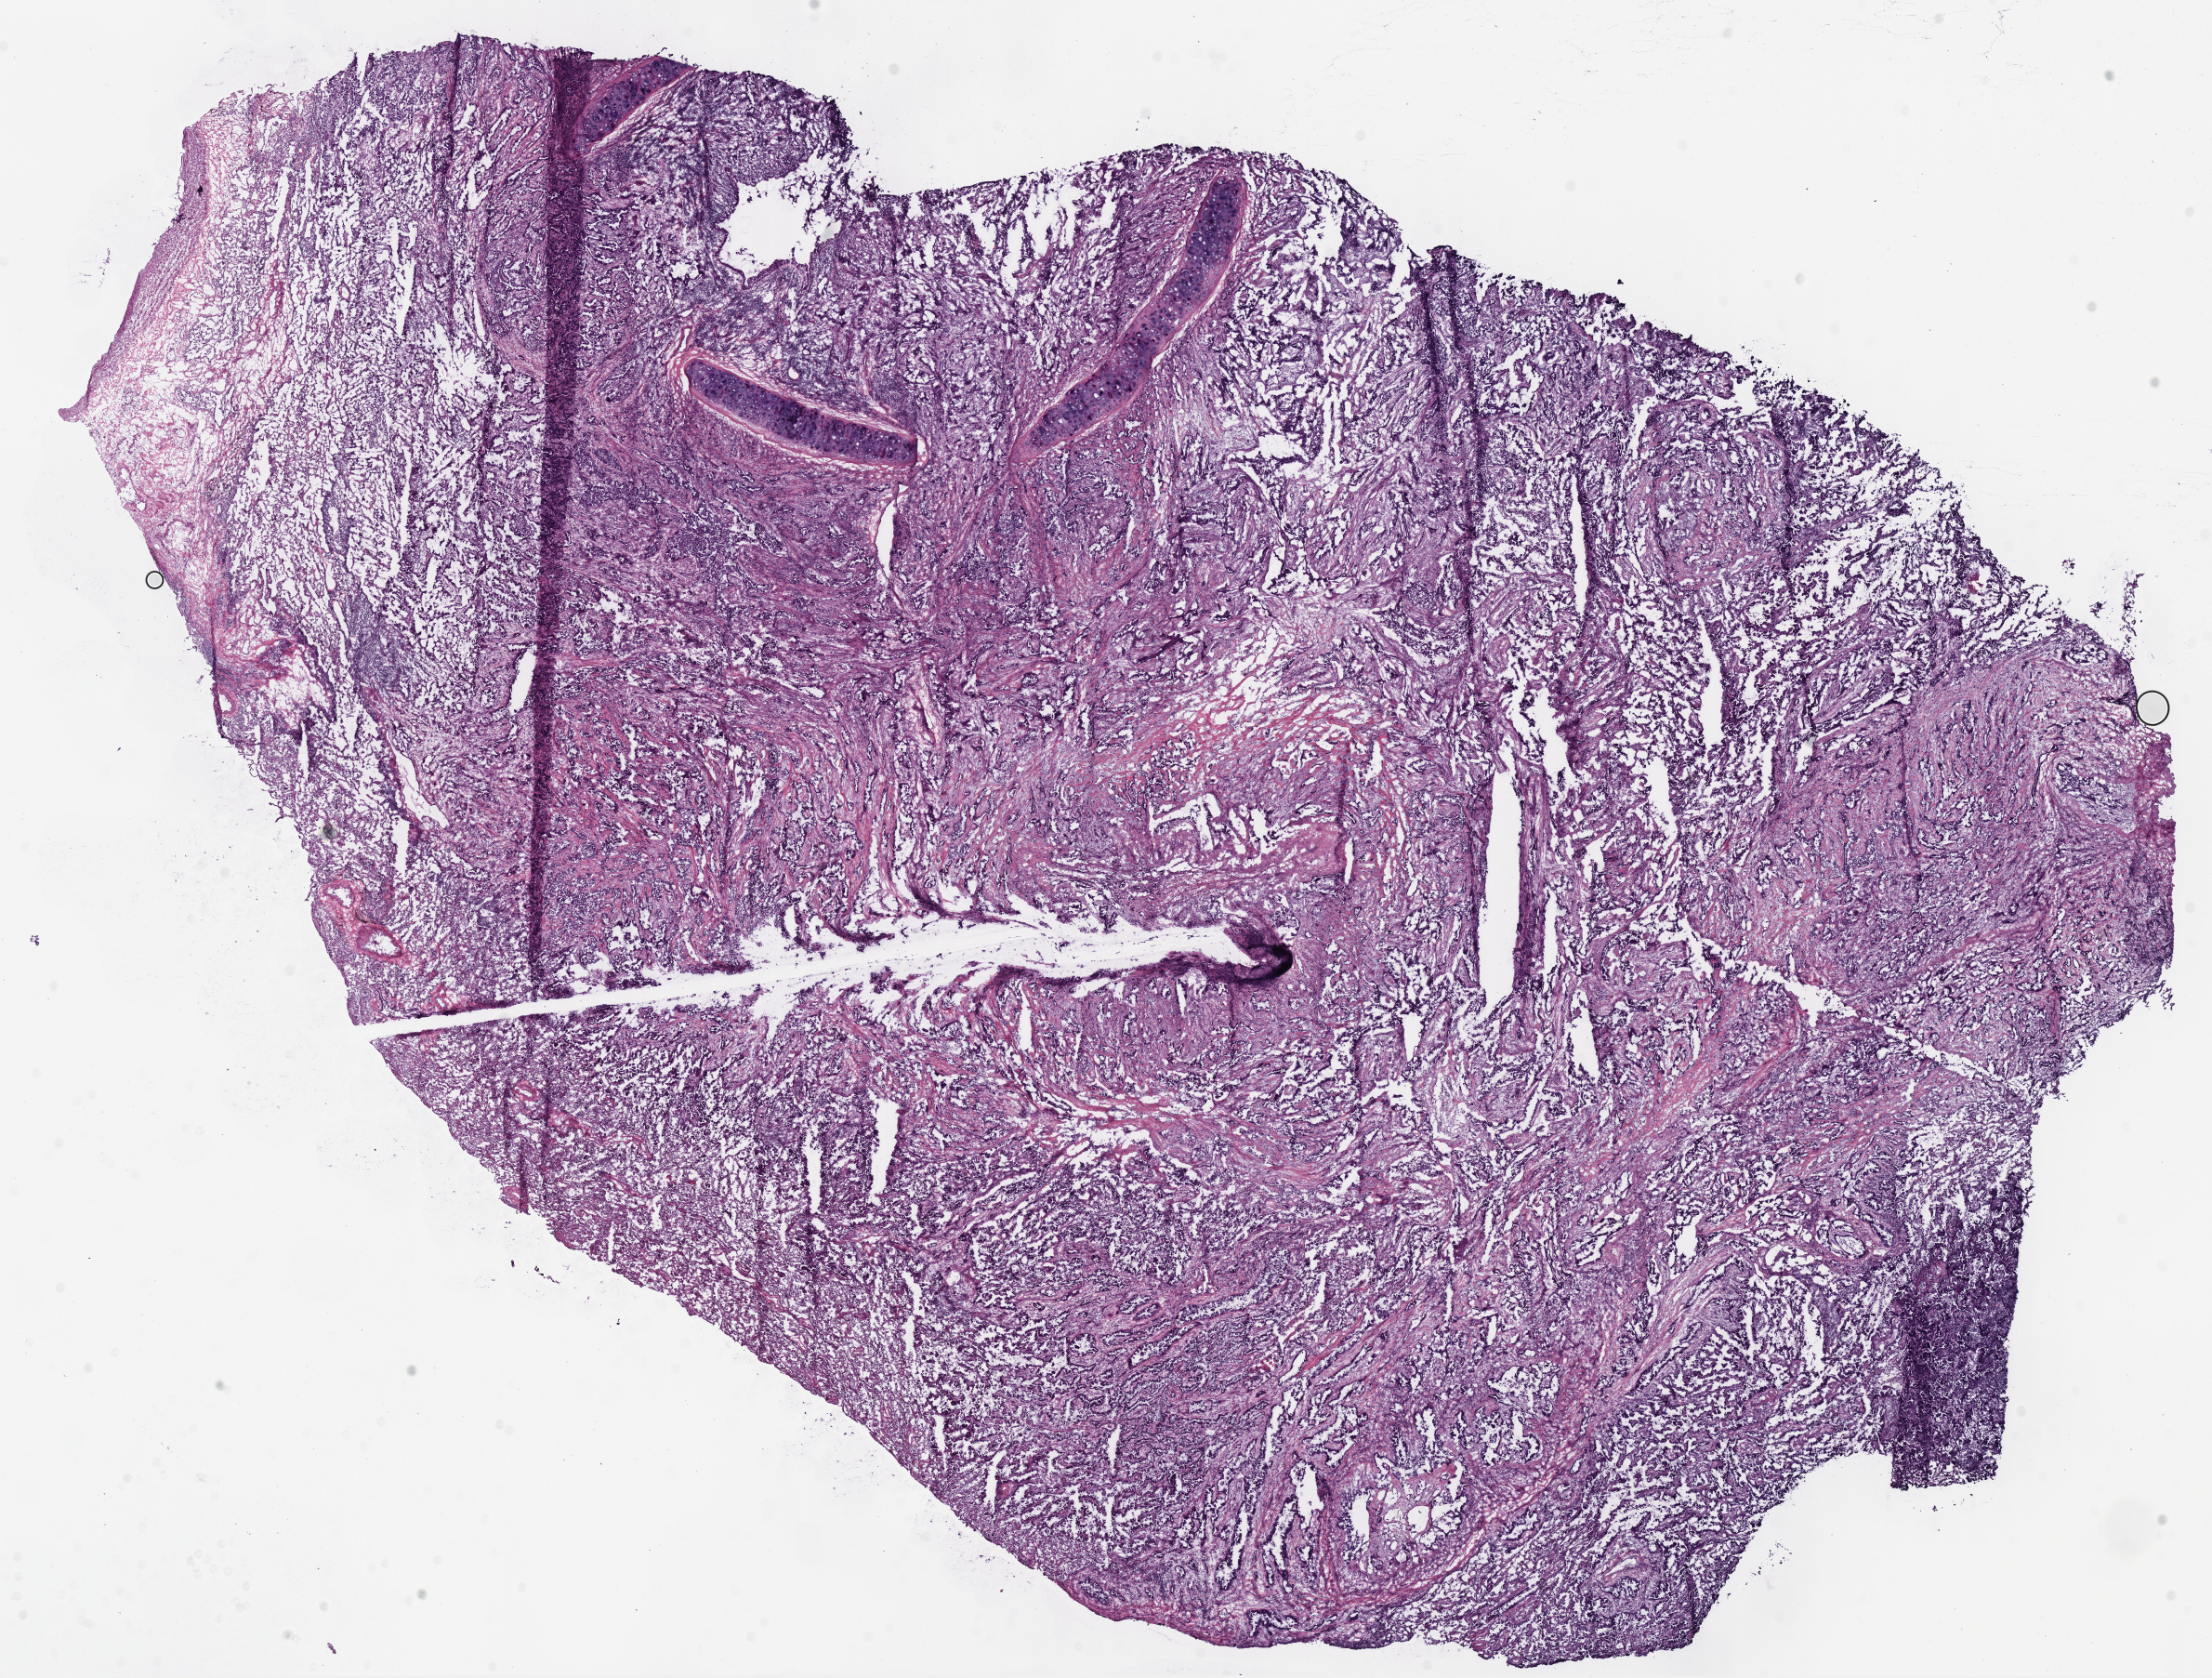
Hematoxylin and eosin (H&E) stained whole-slide image, a low-resolution overview of the entire scanned area, about 18.8 x 14.2 mm (from a 40x scan), frozen section, primary tumour sample from the lung. Patient: female, age at initial diagnosis 62 years. Slide review estimates, as recorded: tumour cells 96%, tumour nuclei 80%, normal cells 2%, stromal cells 0%, necrosis 2%. Inflammatory infiltration, as recorded: lymphocyte infiltration 8%, monocyte infiltration 0%, neutrophil infiltration 0%.
Histologic diagnosis: Papillary adenocarcinoma, NOS (lower lobe, lung). AJCC pathologic stage: IIA (7th edition).